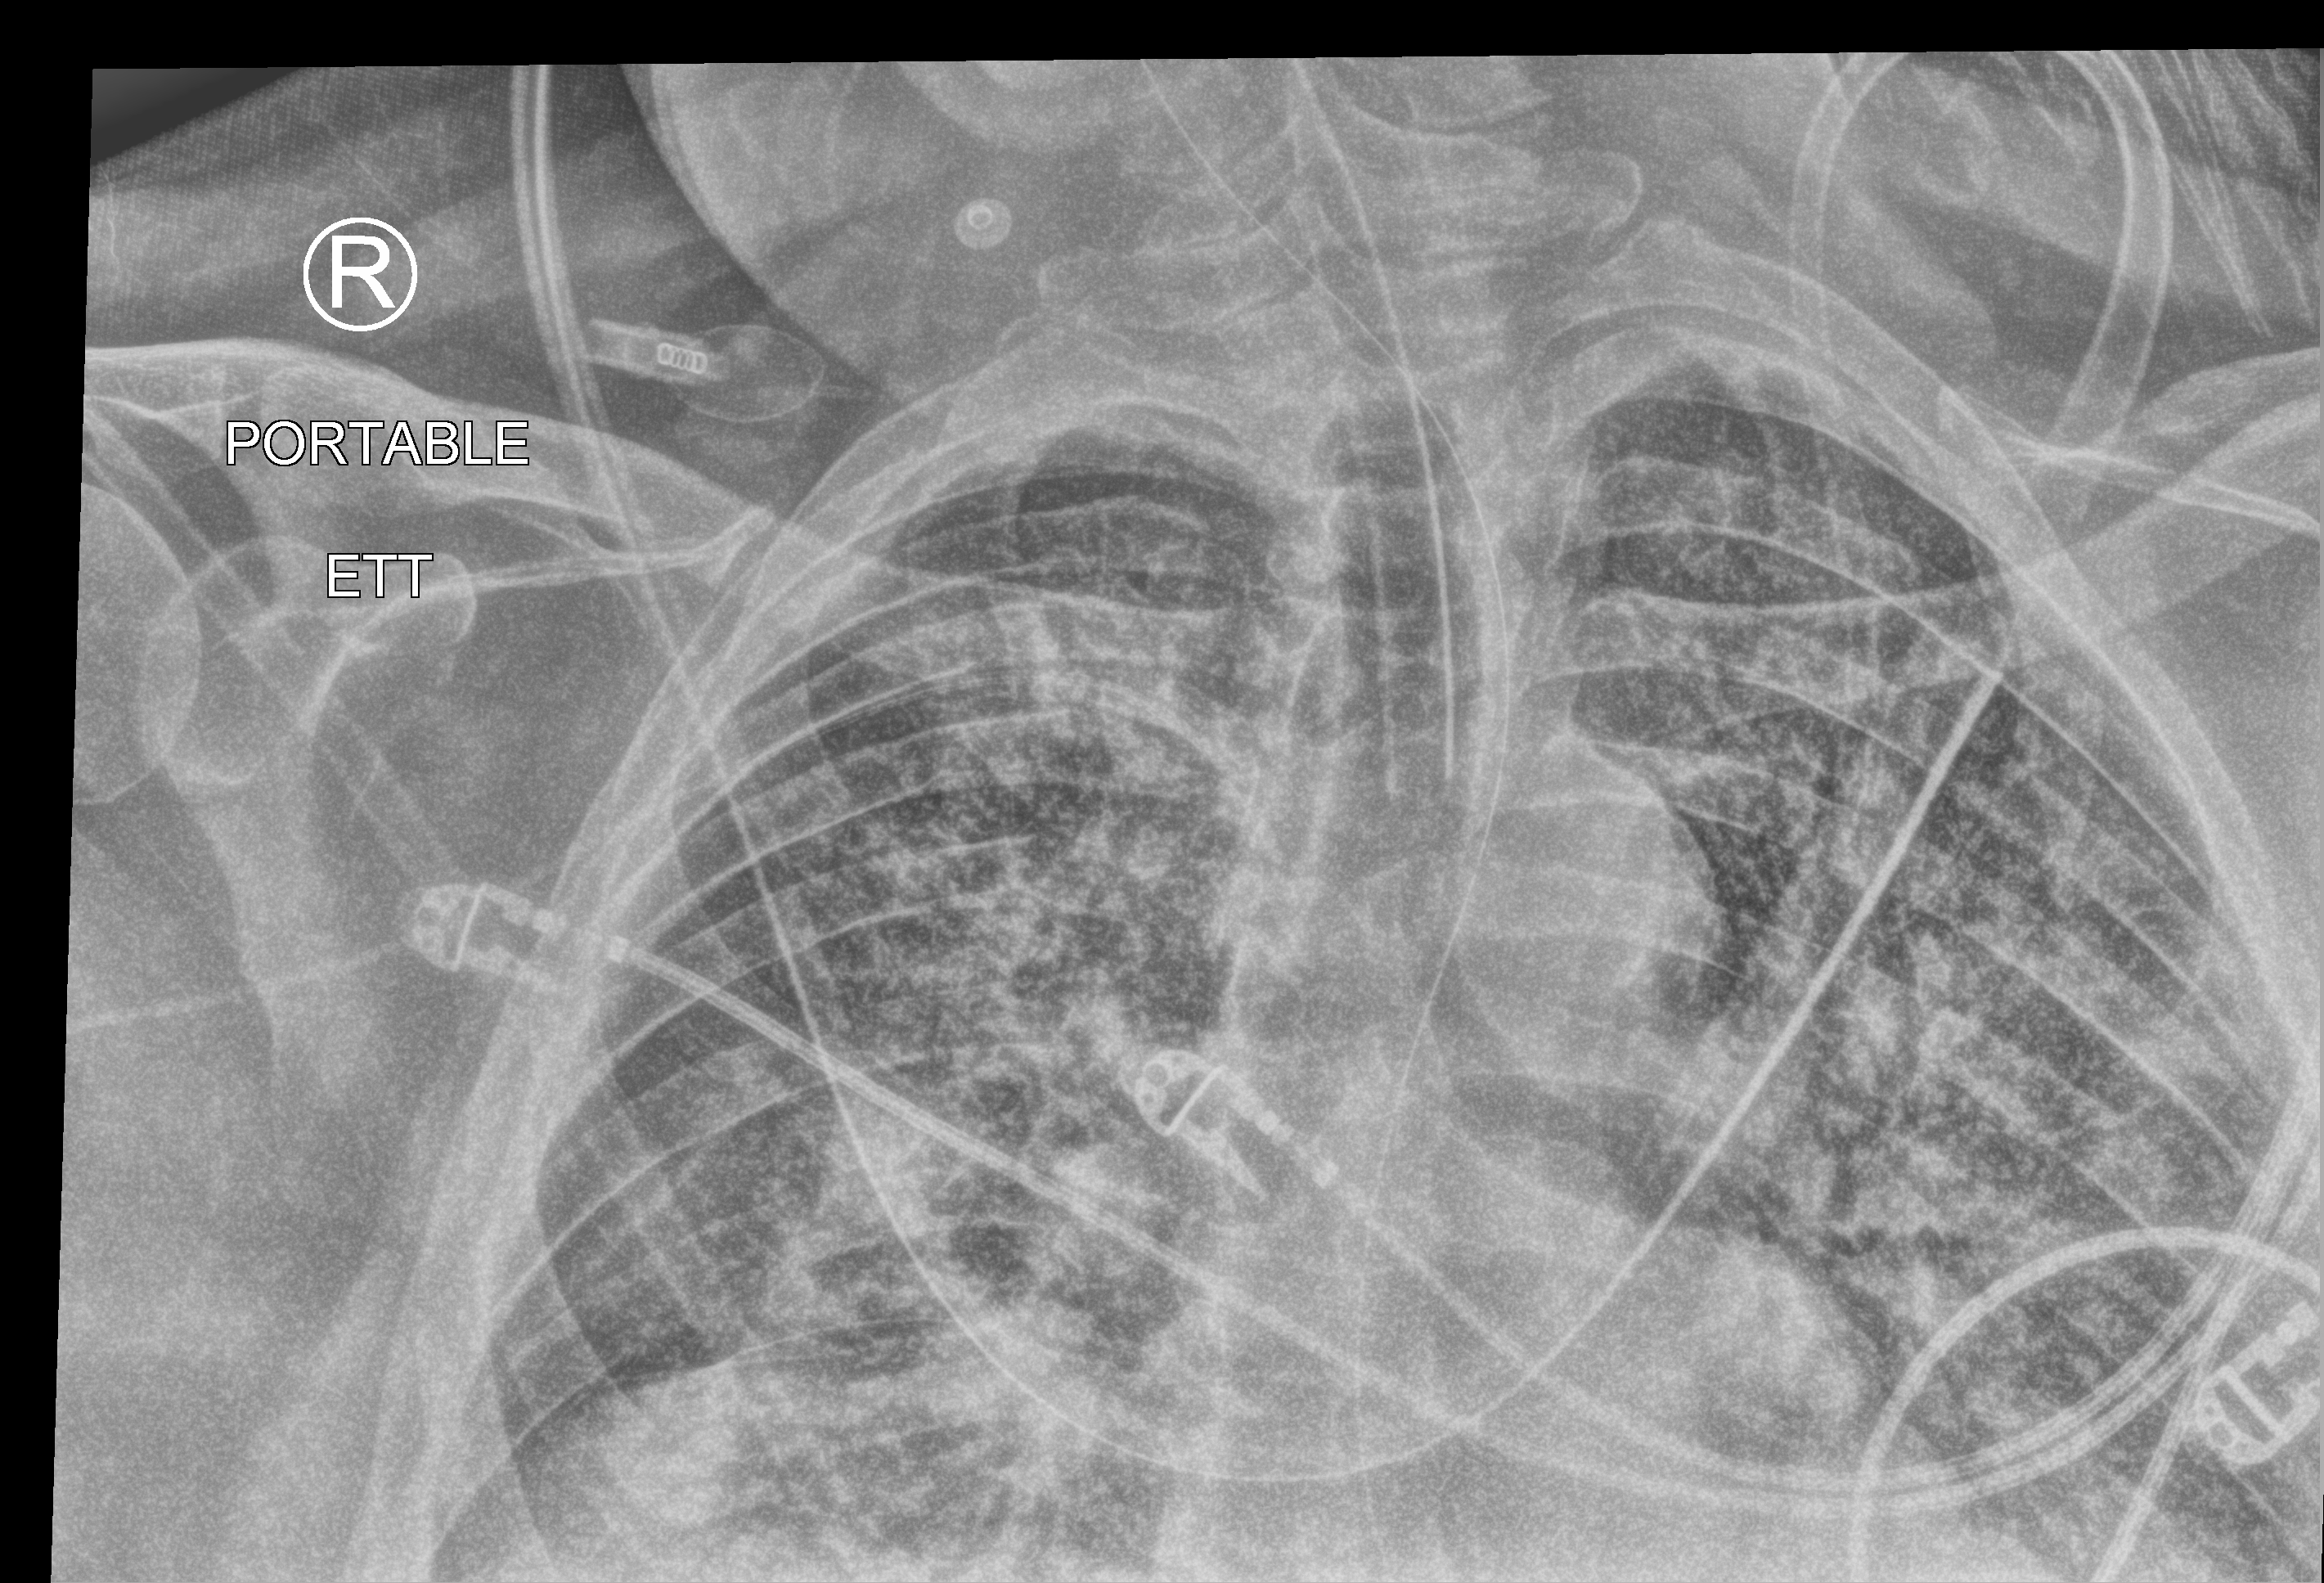
Portable chest radiograph, anteroposterior (AP) projection. Male patient hospitalised with COVID-19, age 60–74 years.
Admission-level facts for this patient (not findings on this image; timing relative to this image not recorded): COPD (admission record): yes.